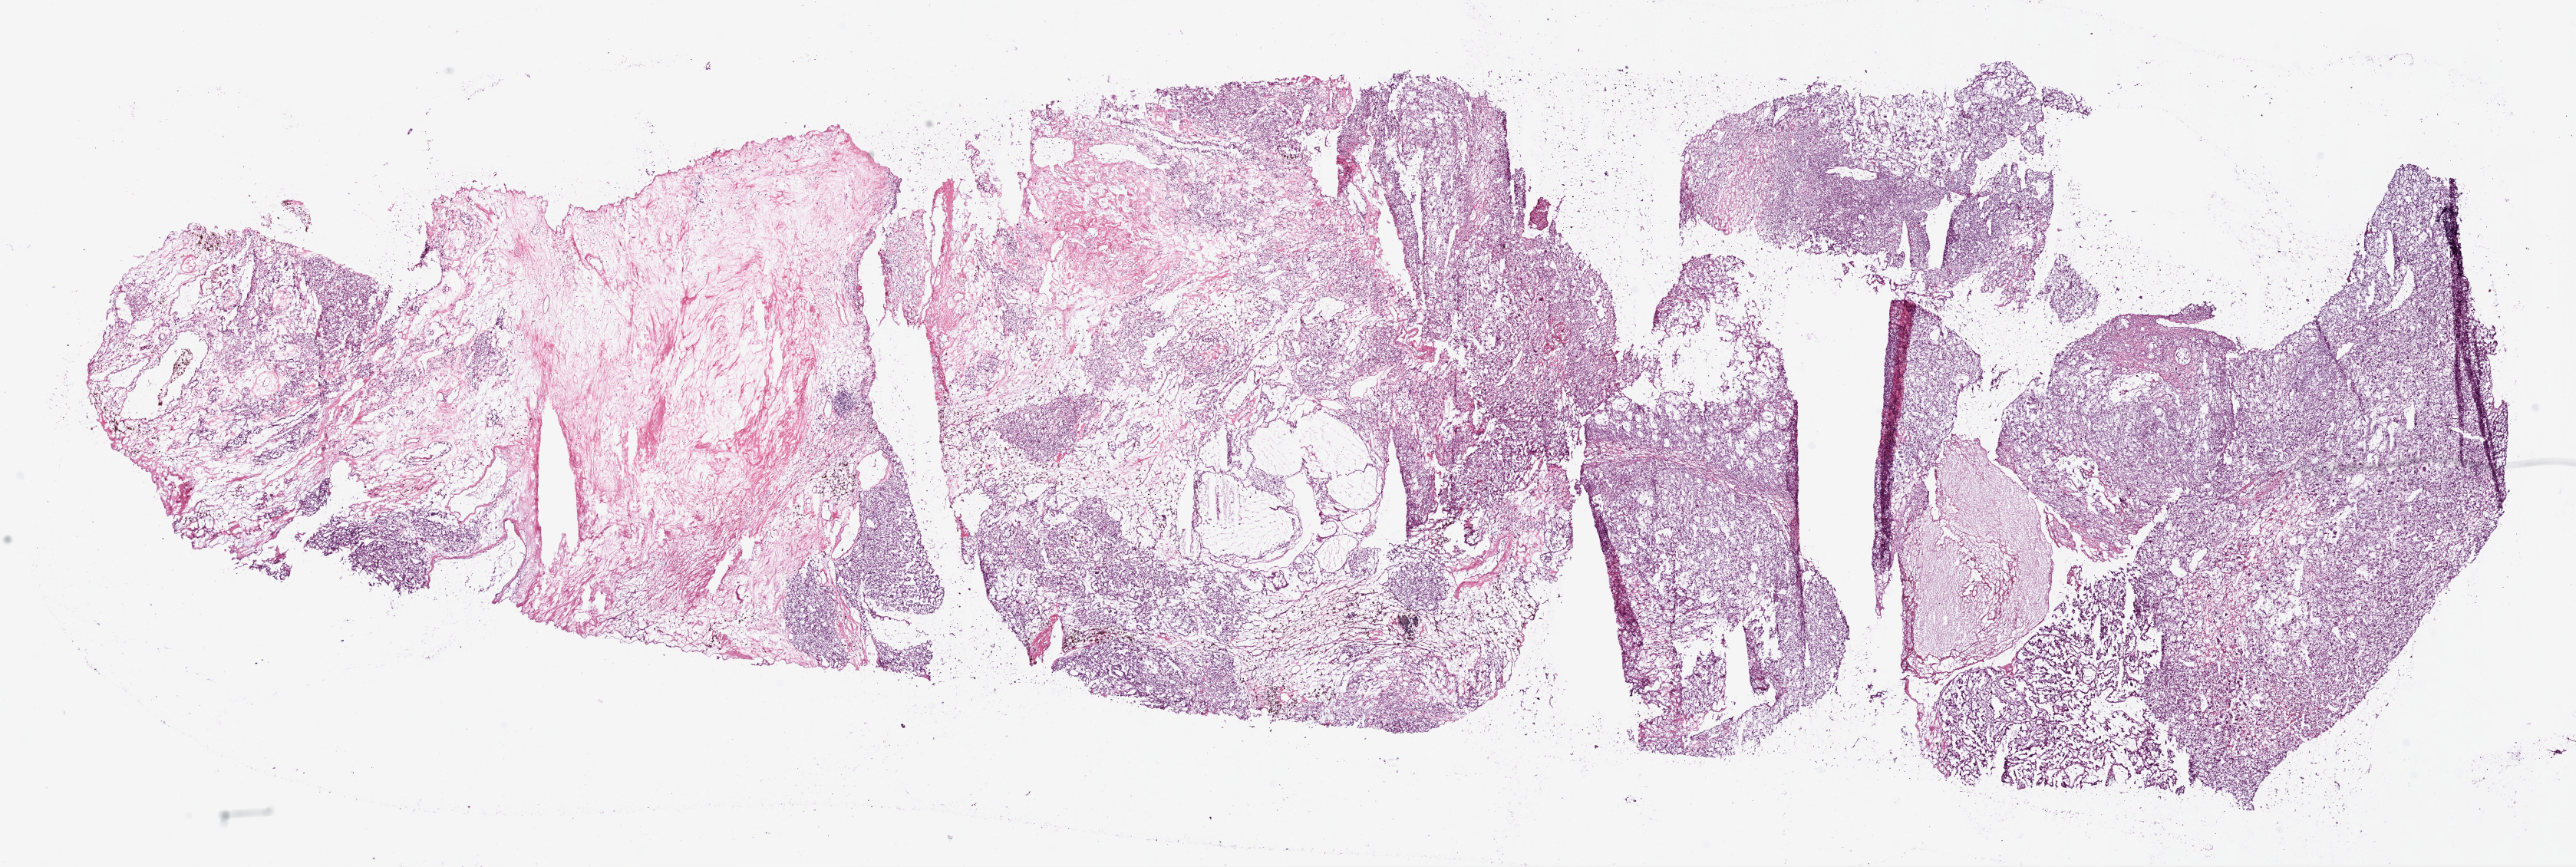
Whole-slide histology image, H&E — whole scanned area (about 27.1 x 9.1 mm, from a 20x scan) shown as a low-resolution overview. Frozen section. Kidney, primary tumour sample. Male patient. Slide review estimates, as recorded: tumour cells 80%, tumour nuclei 75%.
Histologic diagnosis: Clear cell adenocarcinoma, NOS.